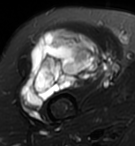
MRI of an extremity soft-tissue mass, one axial slice. T2-weighted fat-saturated. MR volume resampled by the dataset authors to the PET/CT grid (not the native acquisition matrix). 3.27 mm slice thickness. 135 × 146 image matrix. Female patient. Case-level facts recorded for this patient, not image findings: histological type: pleiomorphic undifferentiated sarcoma; grade: high; site of the primary tumour: right quadricep.
Annotated regions visible in this slice (expert contour drawn on MRI and transferred to this co-registered scan by the dataset authors):
- gross tumour volume including surrounding oedema: box from (x=21, y=29) to (x=100, y=108) px
- gross tumour volume (mass): (x=21, y=29)–(x=100, y=108)